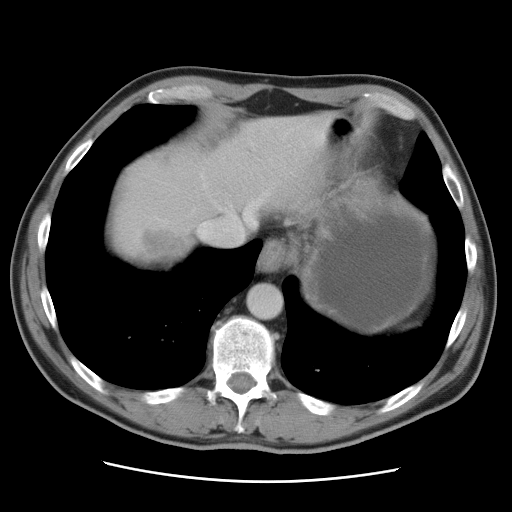
Contrast-enhanced abdominal CT, one axial slice; position 79 of 89 along the scan axis; intravenous contrast given; soft-tissue window (W 400 / L 40 HU); 5 mm slice thickness; 512 × 512 image matrix, field of view 366 × 366 mm. Male patient, age 59 years. From the clinical record (not read from this slice): diagnosis: colorectal cancer liver metastases, imaged before liver resection; multiple liver metastases: yes; largest metastasis: 0.6 cm; disease in both lobes: yes.
Annotated regions visible in this slice (manually delineated by an expert):
- hepatic veins: bounding box (x1, y1, x2, y2) in pixels: (197, 186, 270, 243)
- liver: (107, 113, 331, 270)
- planned liver remnant (the part of the liver to remain after resection): (140, 113, 330, 225)
- liver metastasis: (136, 233, 191, 266)